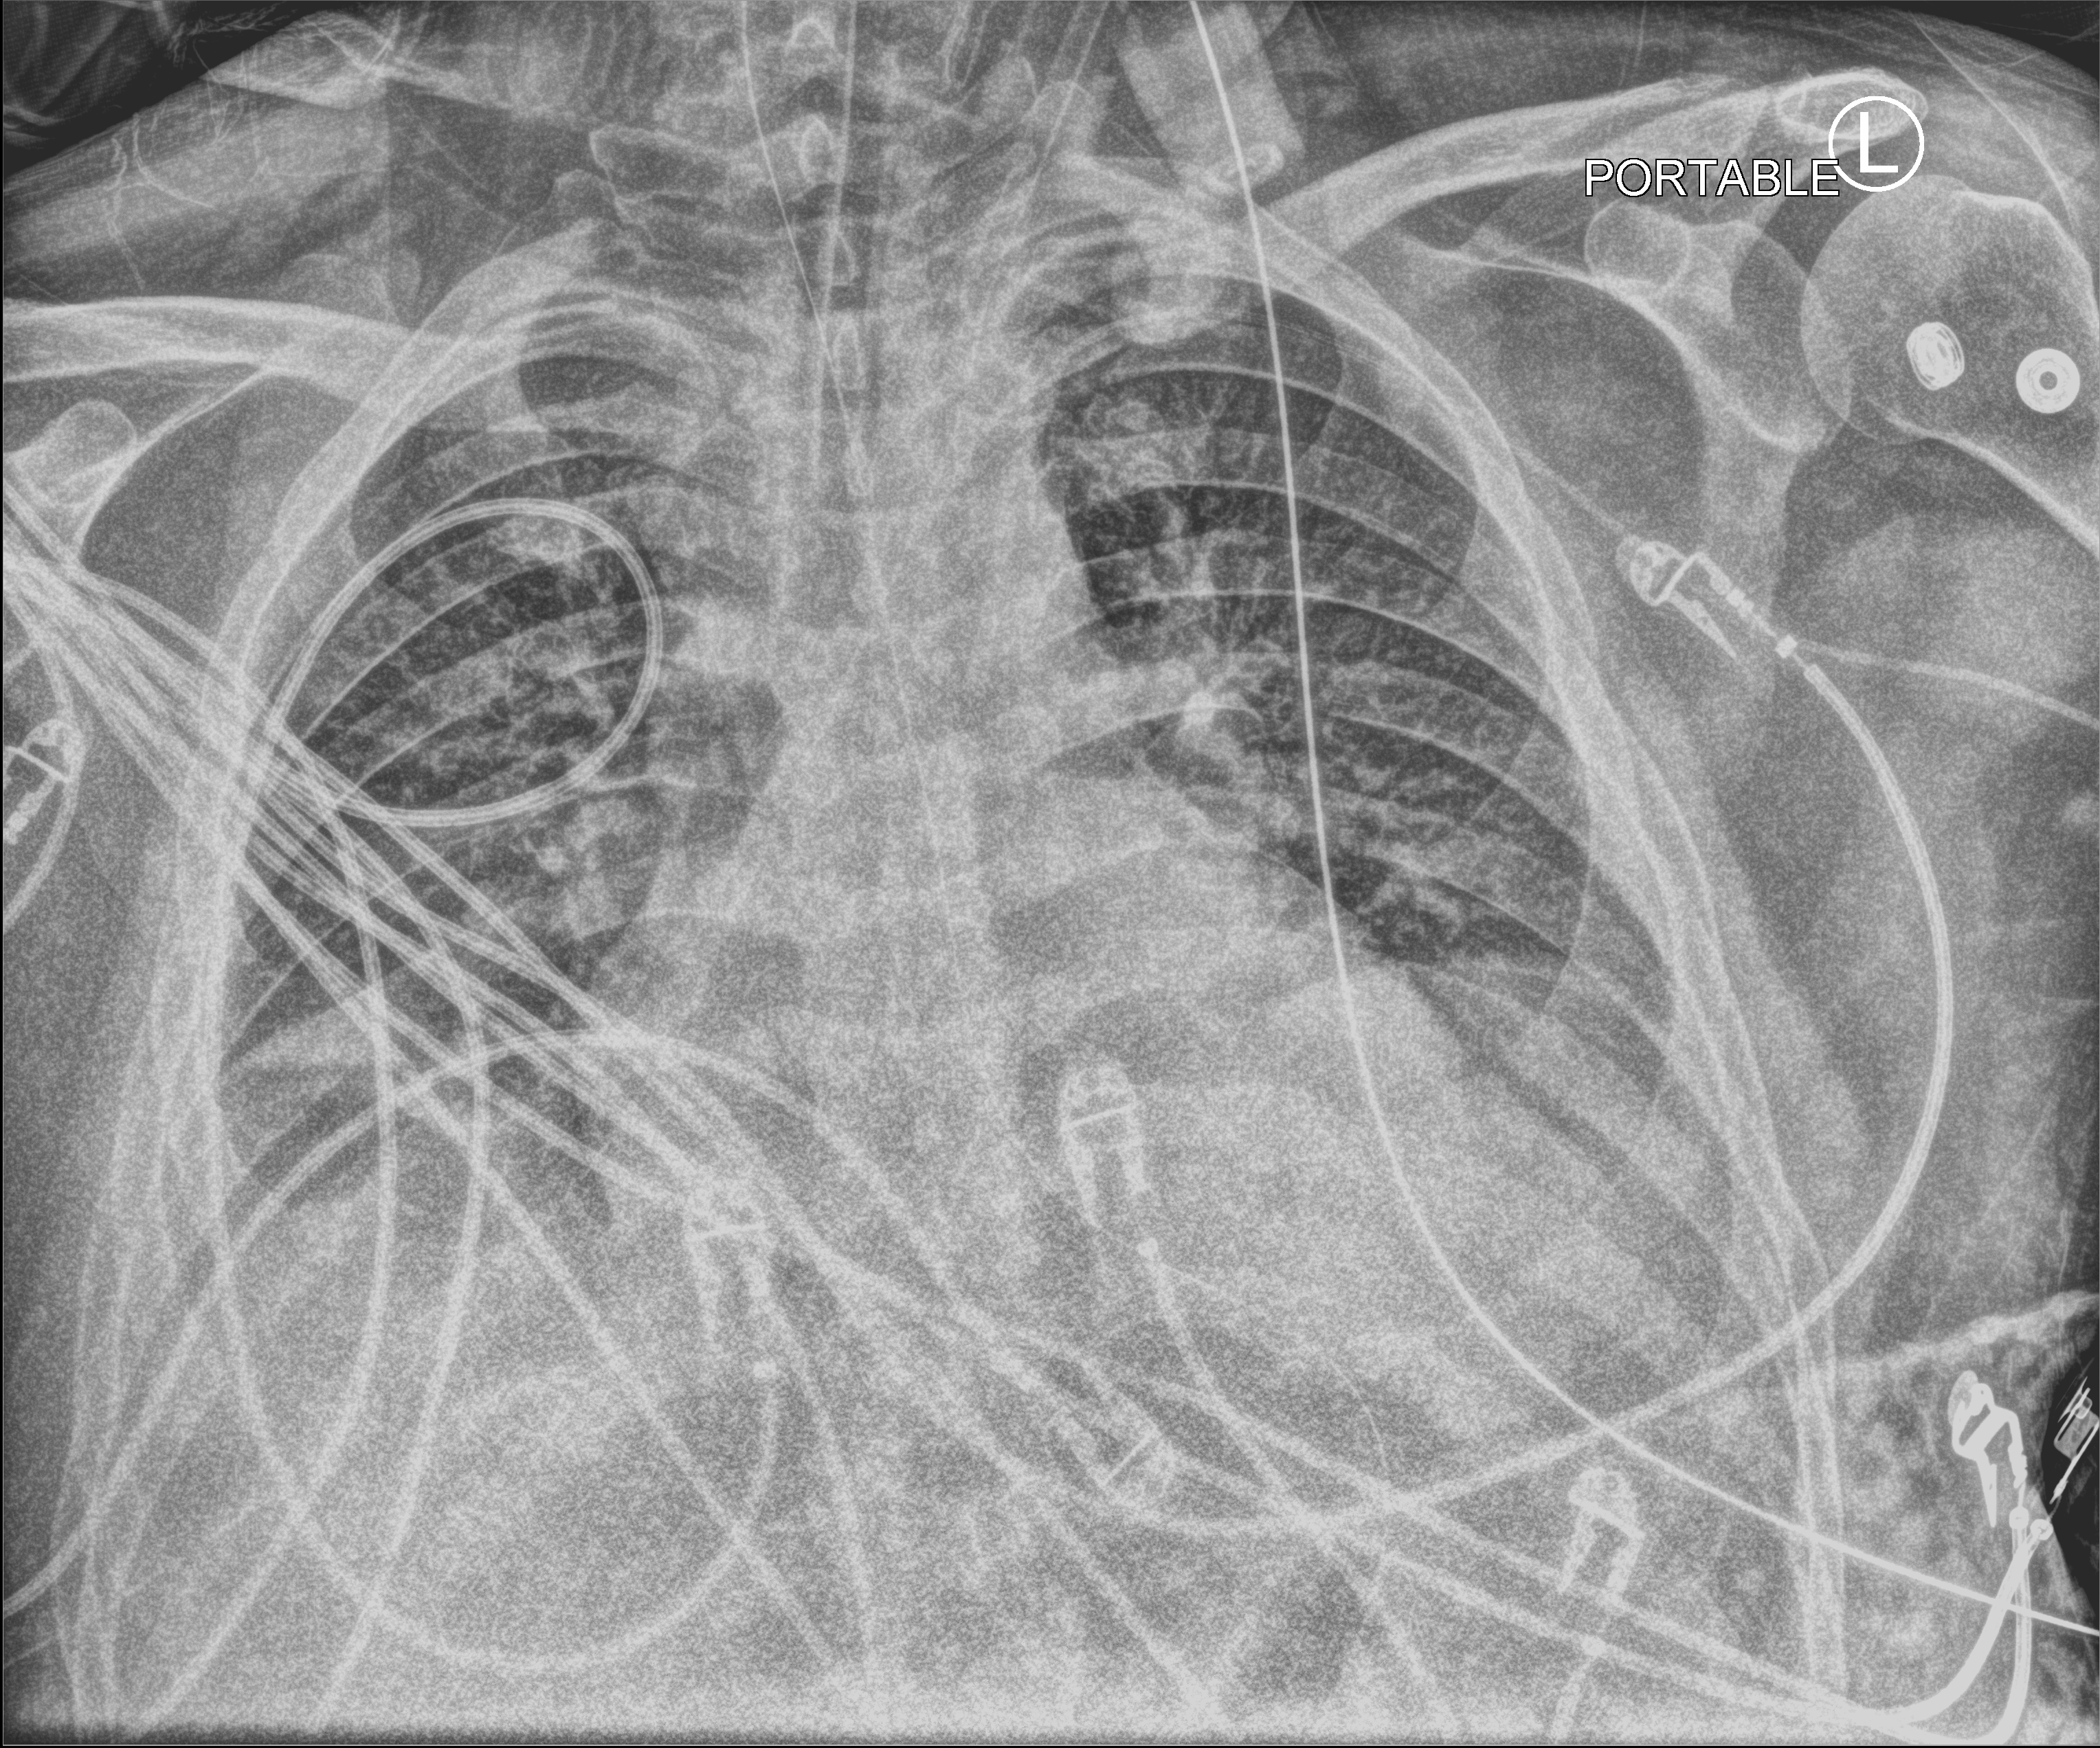
Chest X-ray (portable), anteroposterior (AP) projection. Patient hospitalised with COVID-19; male, aged 18–59 years.
From the hospital-stay record, not from the radiograph (when in the stay this image was taken is not recorded):
- mechanically ventilated during this hospital stay: yes